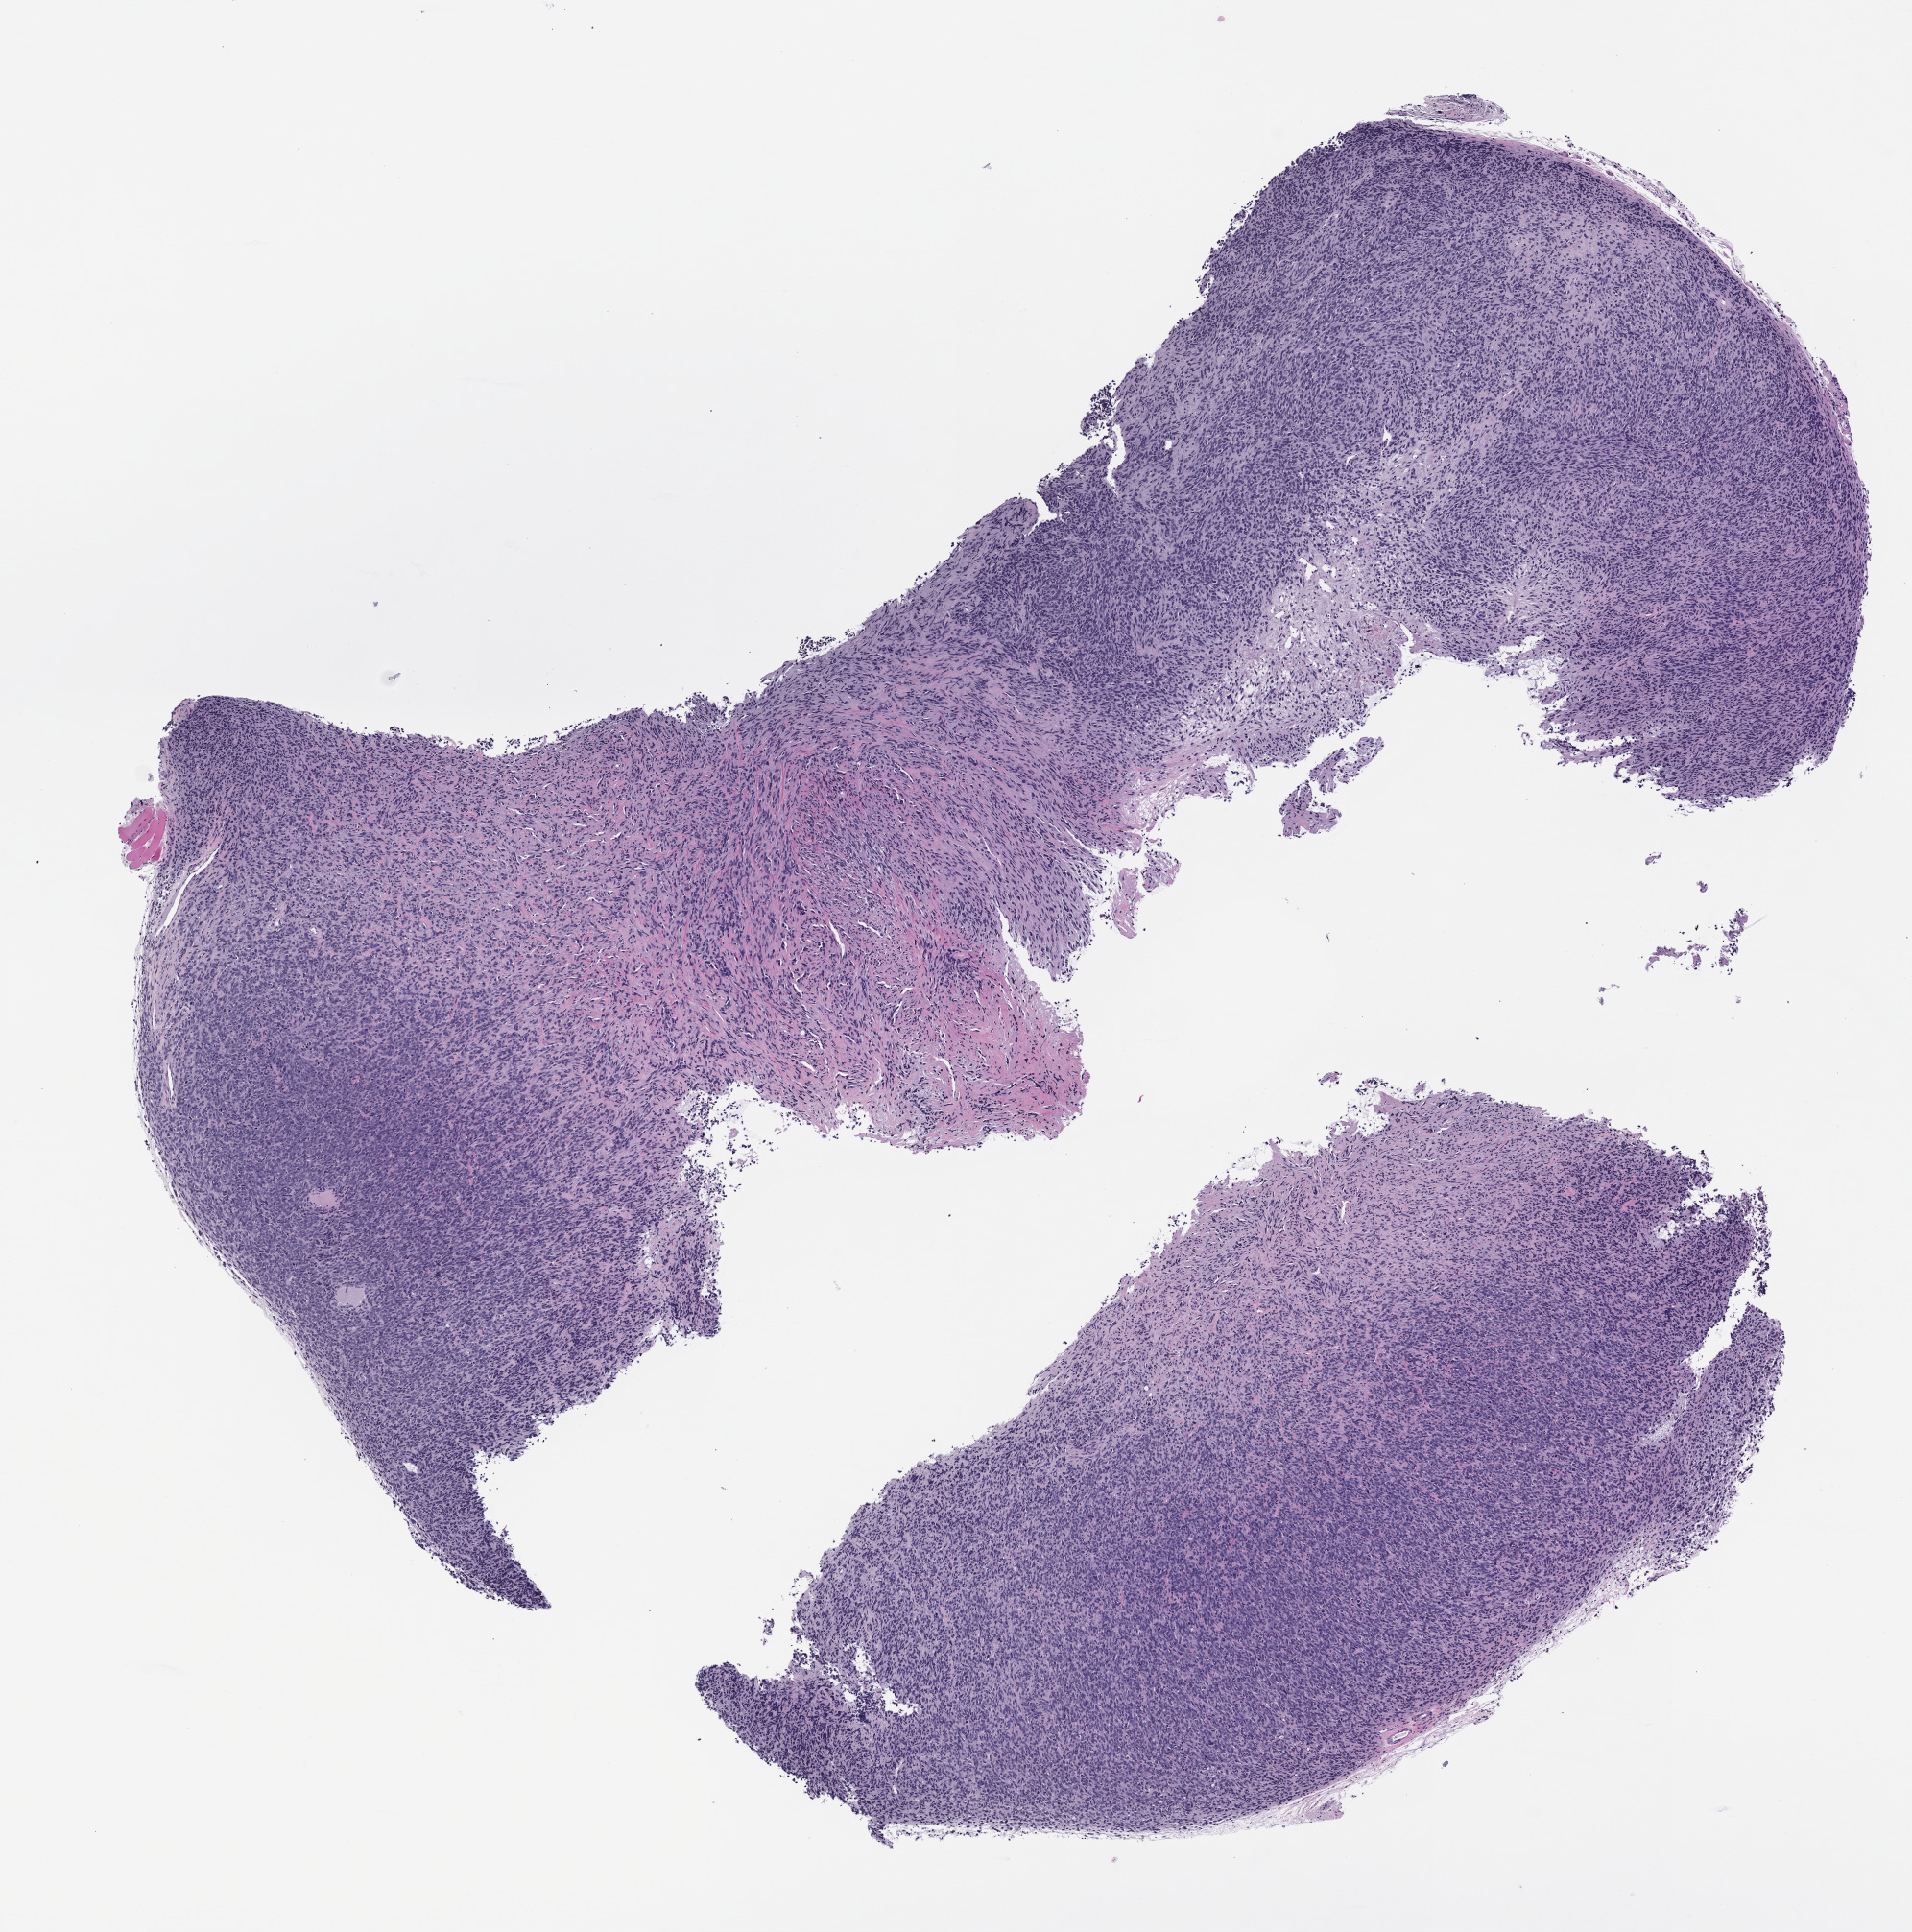
Whole-slide image, haematoxylin and eosin: patient-derived xenograft (human tumor grown in a mouse), passage 1, a low-resolution overview of the entire scanned area, about 8.0 x 8.1 mm, formalin-fixed, paraffin-embedded (FFPE) tissue, tumor site category: musculoskeletal.
Originating patient diagnosis: Spindle Cell Sarcoma.